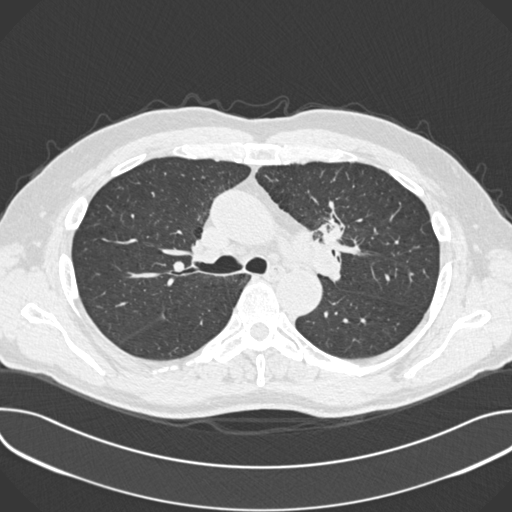
Low-dose screening chest CT, one axial slice. Slice 247 of 361 in the series (ordered by position). 120 kVp. Lung window (W 1500 / L -600 HU). 1 mm slice thickness. 512 × 512 image matrix, field of view 380 × 380 mm.
Structures marked on this image (expert manual segmentation):
- lesion 1 (tumor, upper lobe of left lung): bounding box [x1, y1, x2, y2] px = [318, 216, 344, 245]